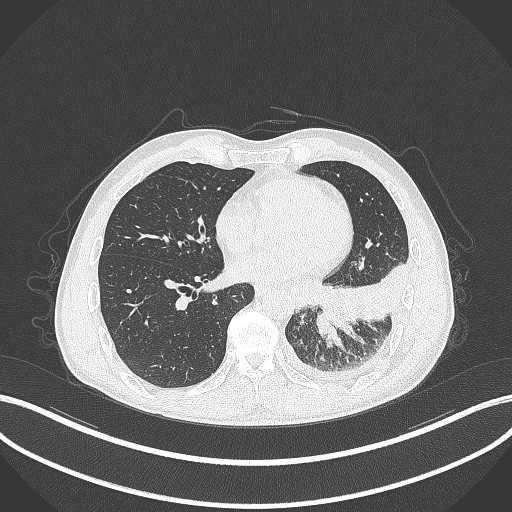
Chest CT, one axial slice; slice 119 of 295 in the series (ordered by position); reconstruction kernel B70f; lung window (W 1500 / L -600 HU); 512 × 512 image matrix, field of view 400 × 400 mm. Patient: male, 47 years. From the clinical record (not read from this slice): clinical TNM (as recorded): T3 N1 M1c; histopathological grade: G3.
Structures marked on this image (rectangle marked by the reading radiologist):
- lung tumour (recorded histology: small cell carcinoma): box from (x=313, y=307) to (x=342, y=335) px